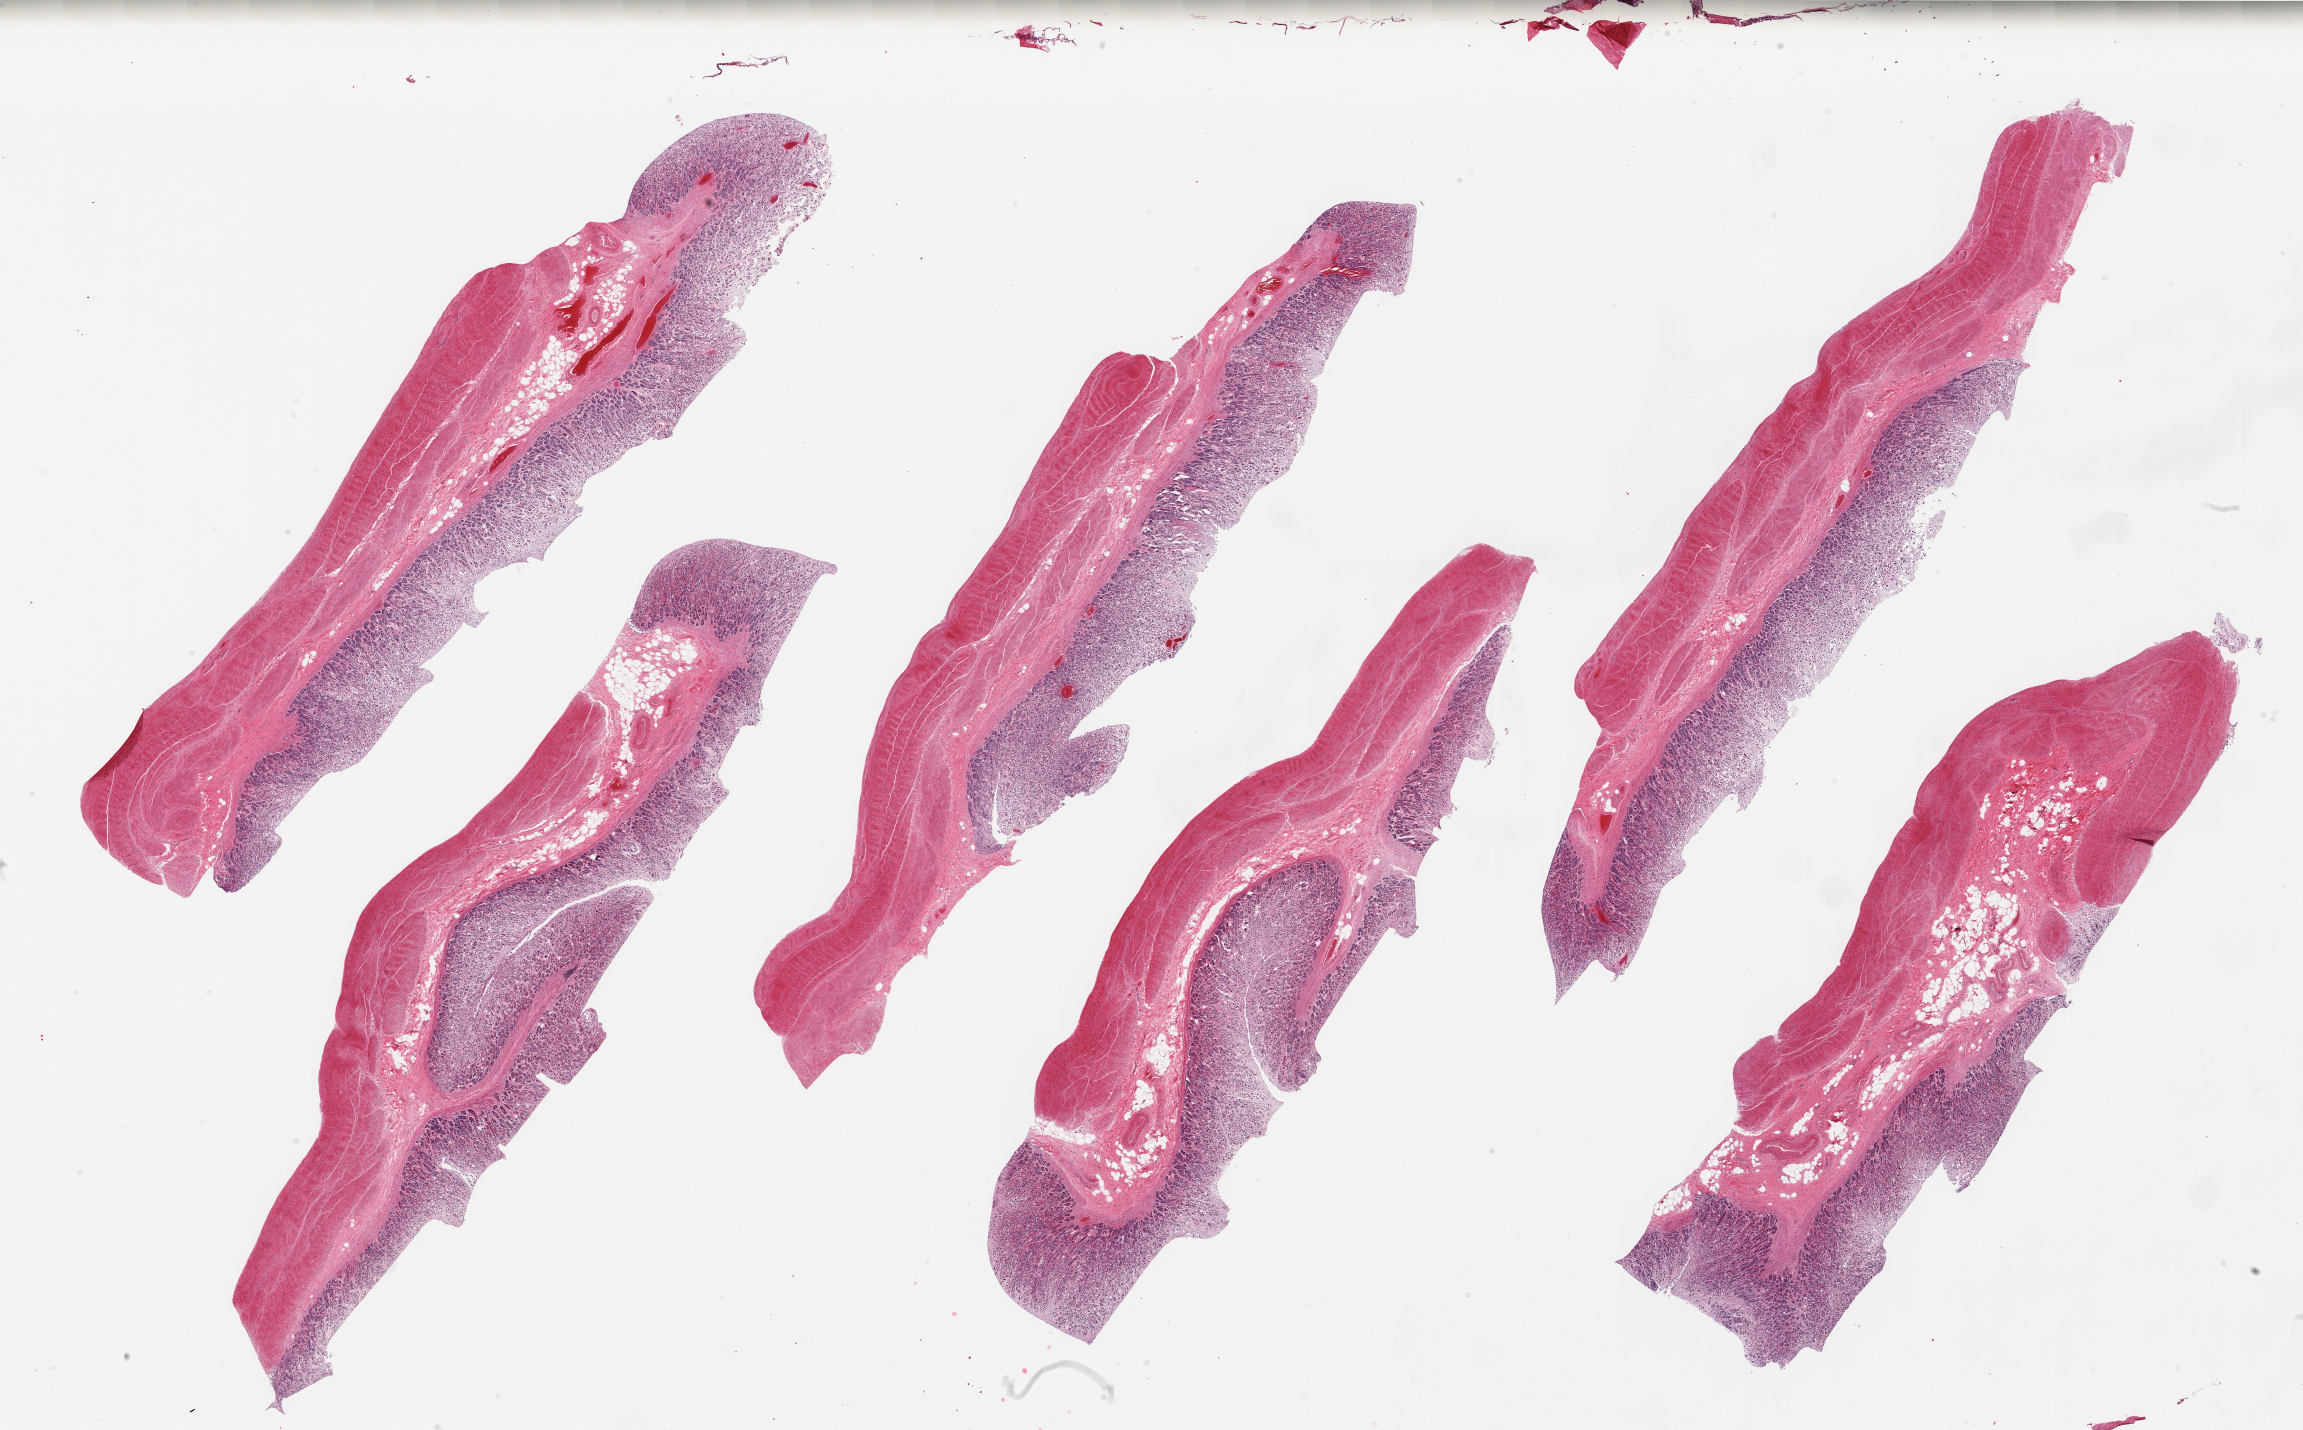
Hematoxylin and eosin (H&E) whole-slide image, whole scanned area (about 36.4 x 22.6 mm) shown as a low-resolution overview, PAXgene-fixed, paraffin-embedded tissue, target tissue: stomach, donor tissue sample. Donor sex: male.
Review note (as recorded): 6 pieces; mucosal autolysis grade 3; muscle intact; congestion, well trimmed.